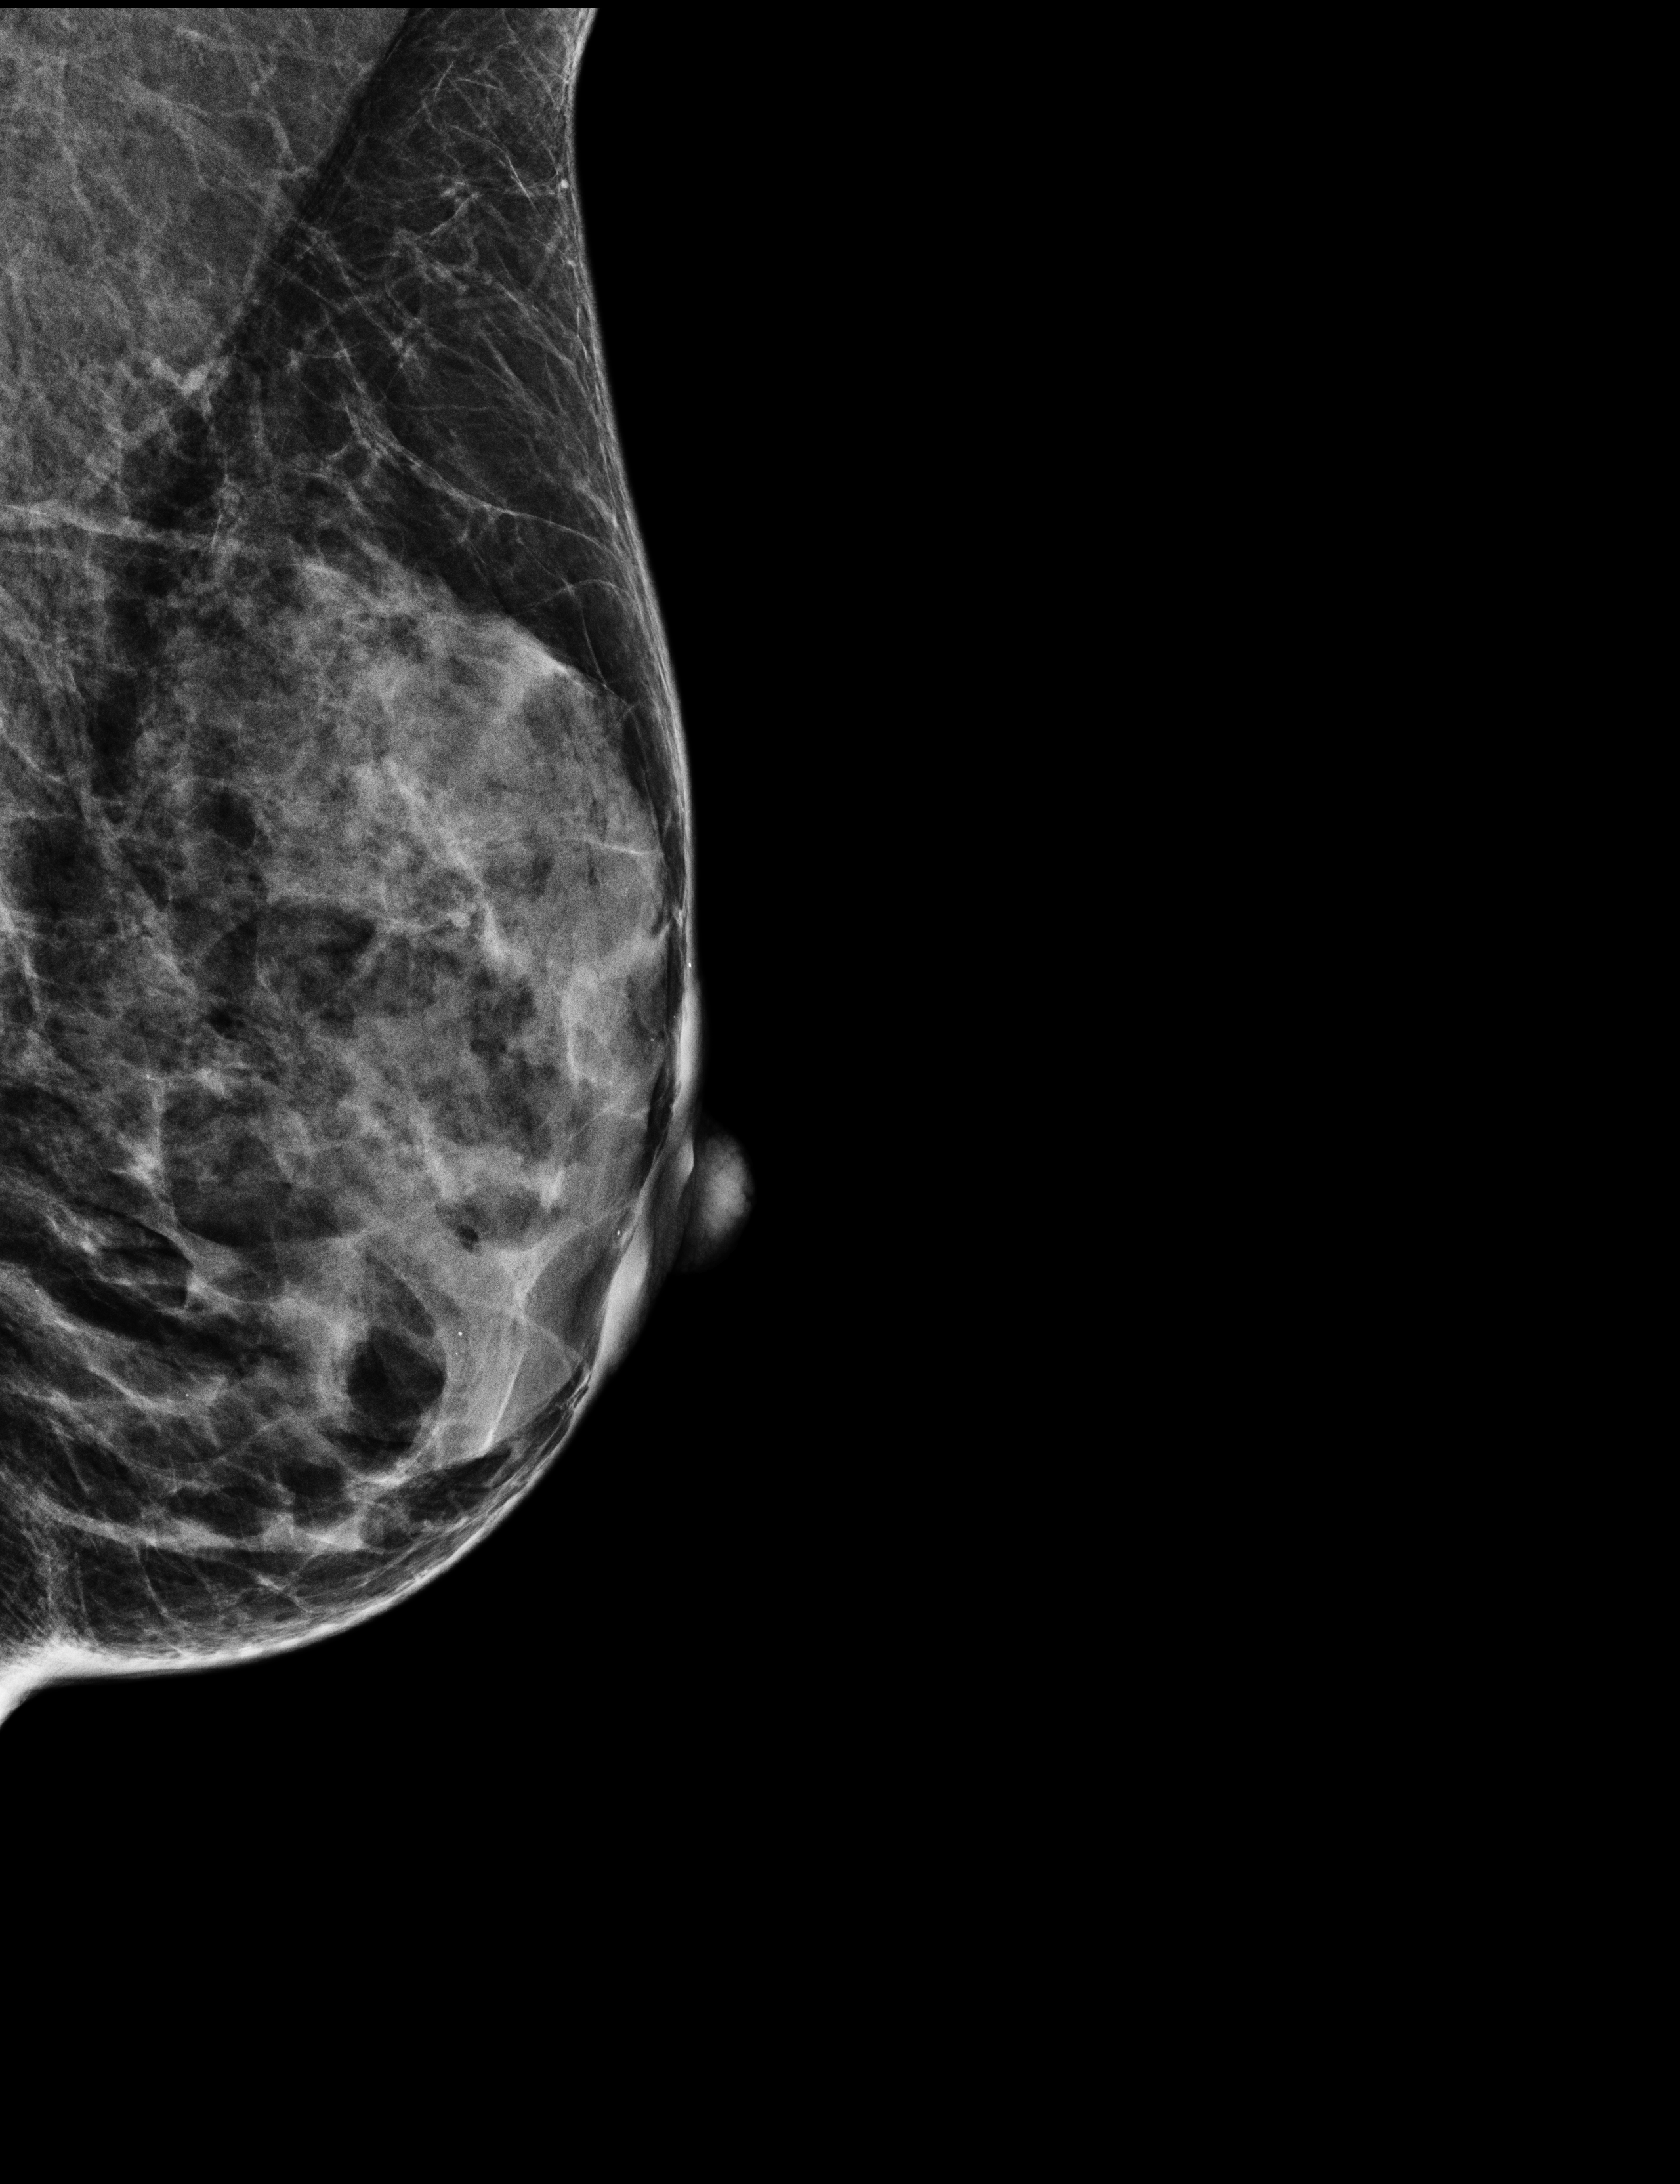
Digital mammogram (FFDM), left breast, mediolateral oblique (MLO) view, annual screening mammography examination. Female patient, age 56 years.
BI-RADS breast density category at the screening exam (both breasts, scale 1–4): 3. Final BI-RADS assessment for this screening round (tomosynthesis exam, both breasts): category 2. Recall: recalled for additional imaging after this screen.